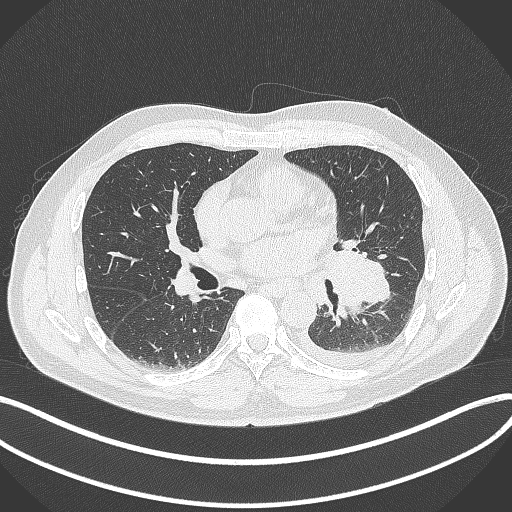
Chest CT, one axial slice. Position 184 of 342 along the scan axis. Reconstruction kernel B70f. Lung window (W 1500 / L -600 HU). 1 mm slice thickness. 512 × 512 image matrix, field of view 400 × 400 mm. Male patient, age 58 years. Case-level facts recorded for this patient, not image findings: clinical TNM (as recorded): T3 N1 M1b.
Outlined on this slice (rectangle marked by the reading radiologist):
- lung tumour (recorded histology: small cell carcinoma): bounding box [x1, y1, x2, y2] px = [322, 236, 388, 312]